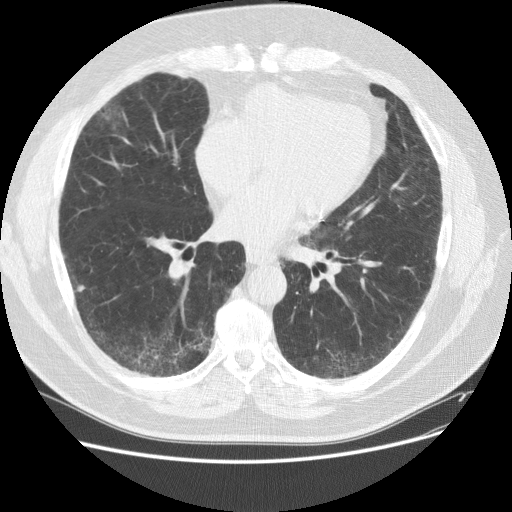
Low-dose screening chest CT, one axial slice. Slice 74 of 151 in the series (ordered by position). Reconstruction kernel STANDARD. 120 kVp. Lung window (W 1500 / L -600 HU). 2.5 mm slice thickness. 512 × 512 image matrix, field of view 378 × 378 mm.
Annotated regions visible in this slice (outlined manually by an expert reader):
- lesion 1 (tumor, lower lobe of right lung): bounding box (x1, y1, x2, y2) in pixels: (76, 284, 86, 295)